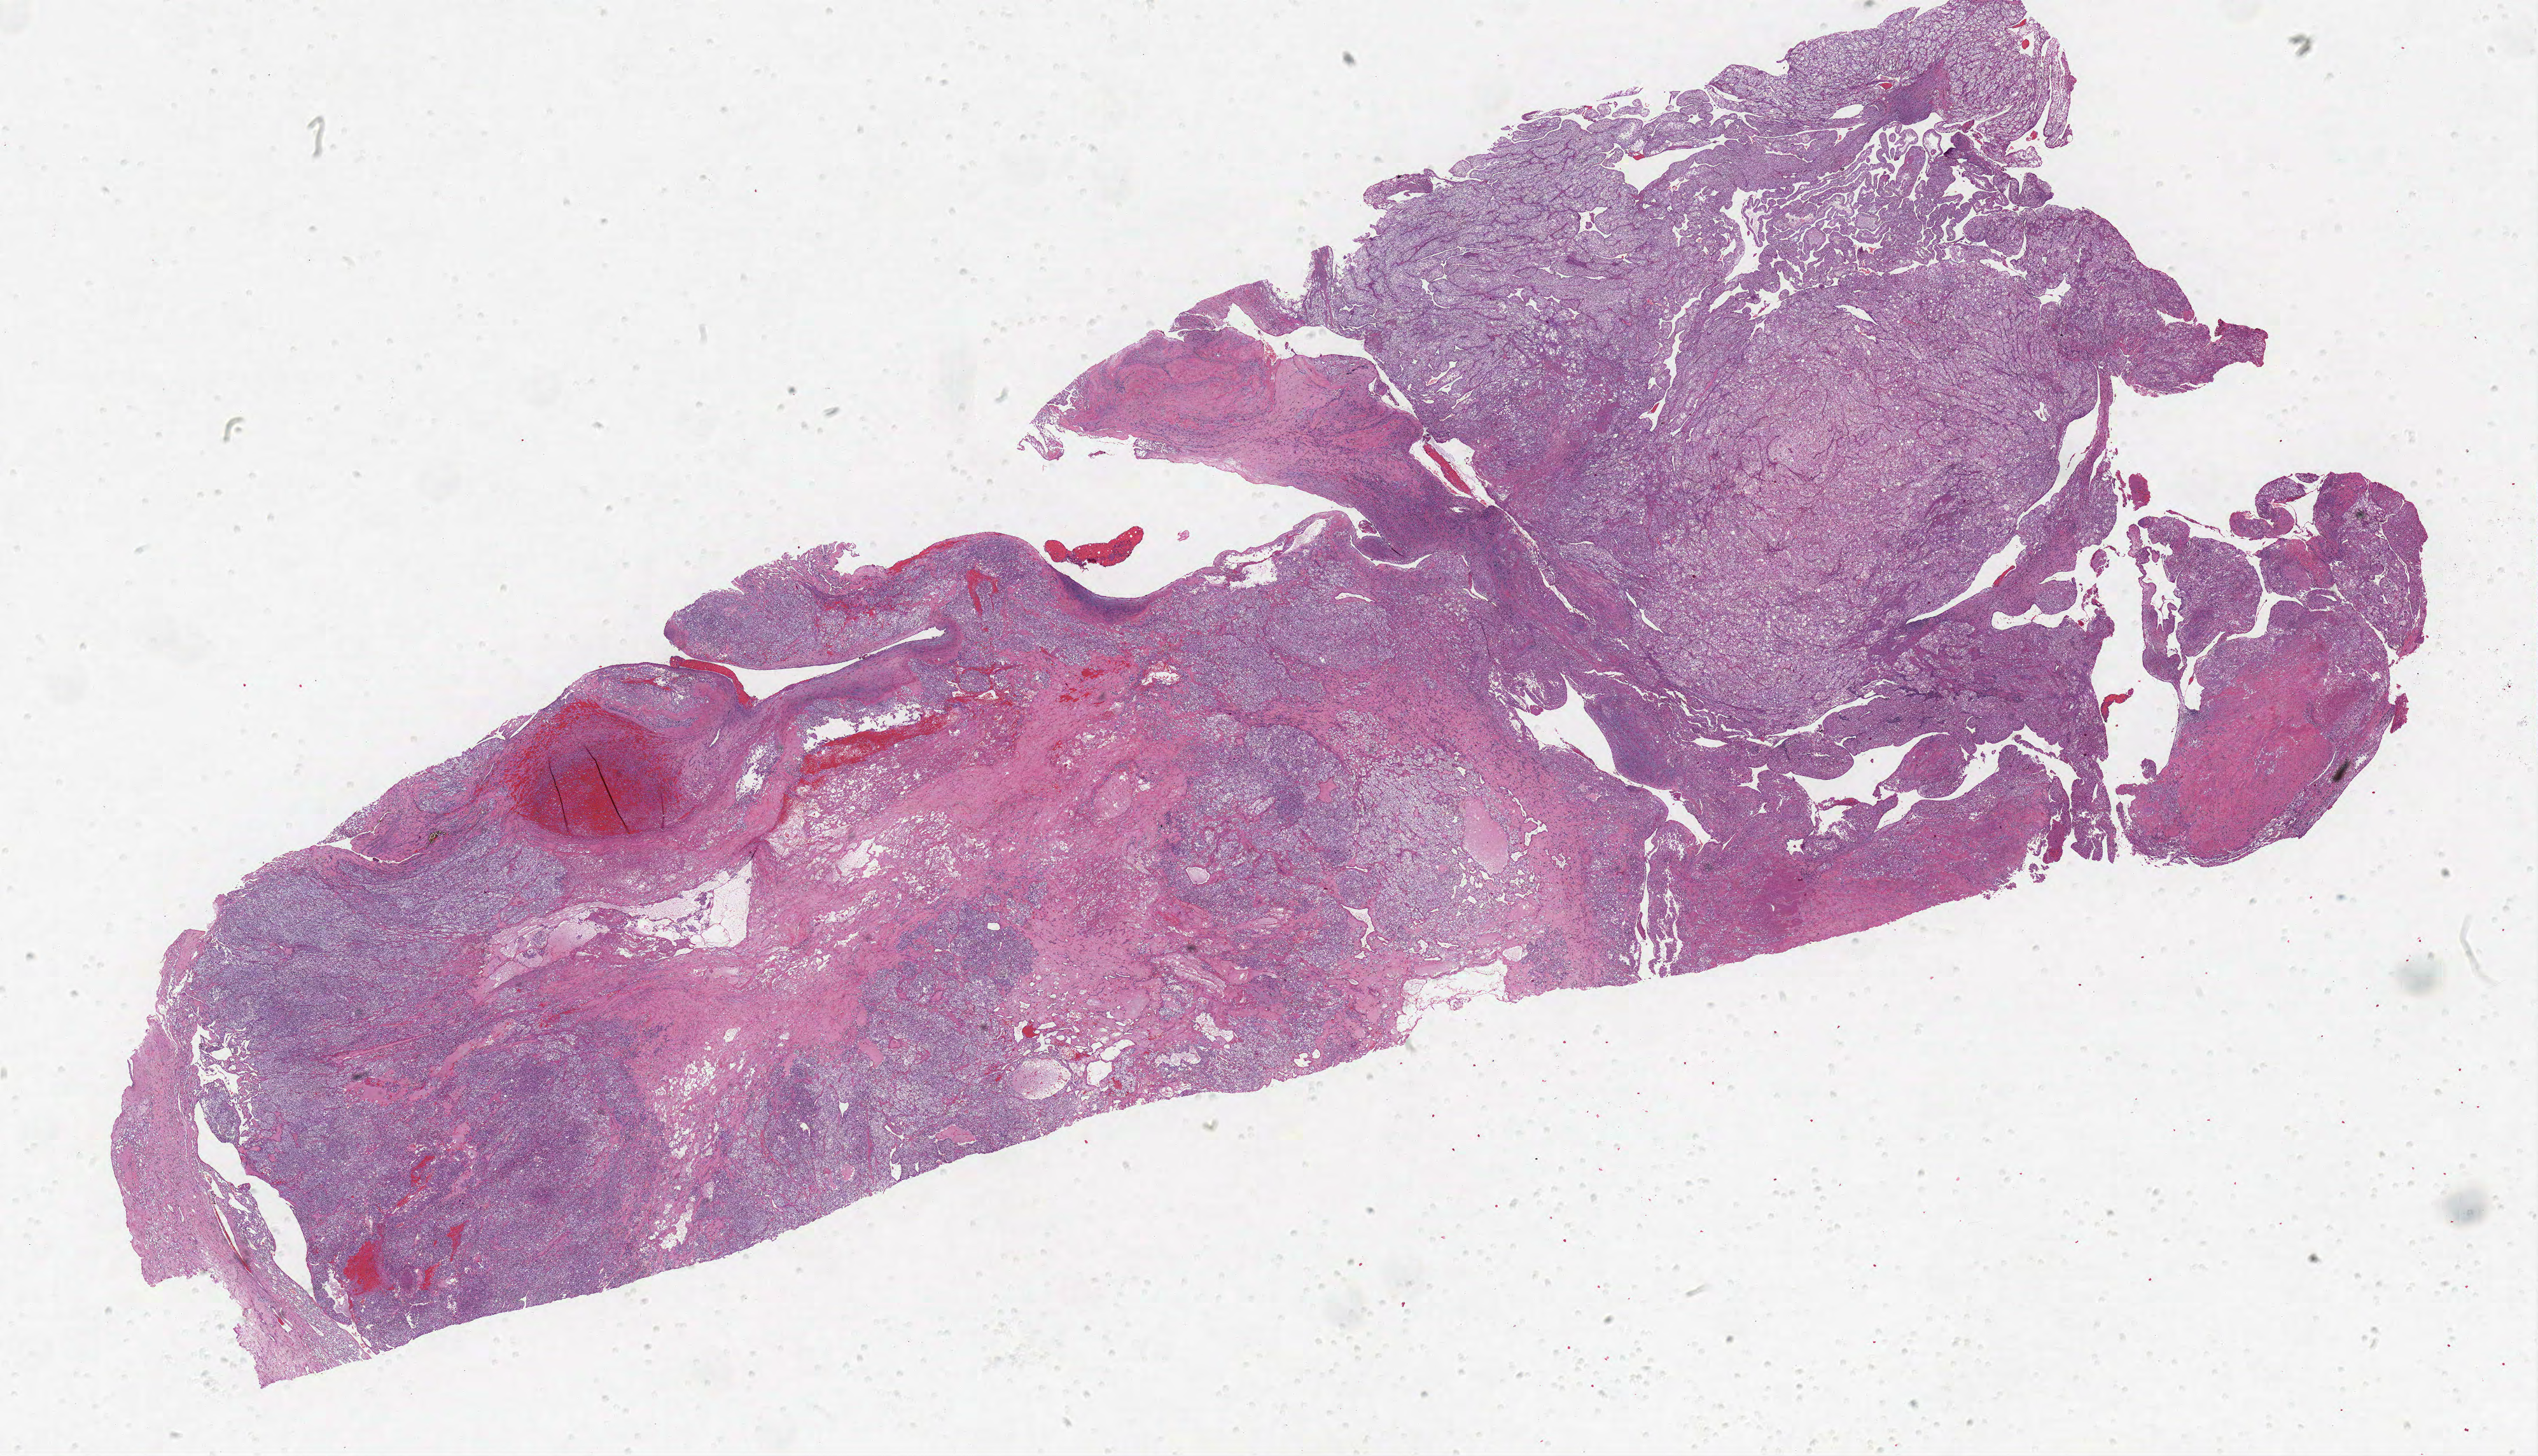
Hematoxylin and eosin (H&E) stained whole-slide image — low-resolution overview of the scanned area, about 31.9 x 18.3 mm, formalin-fixed paraffin-embedded (FFPE) diagnostic section, sample: primary tumour, kidney. Female patient; age at initial diagnosis 59 years. Histologic grade: G4 (undifferentiated).
* diagnosis: Clear cell adenocarcinoma, NOS
* AJCC pathologic stage: III